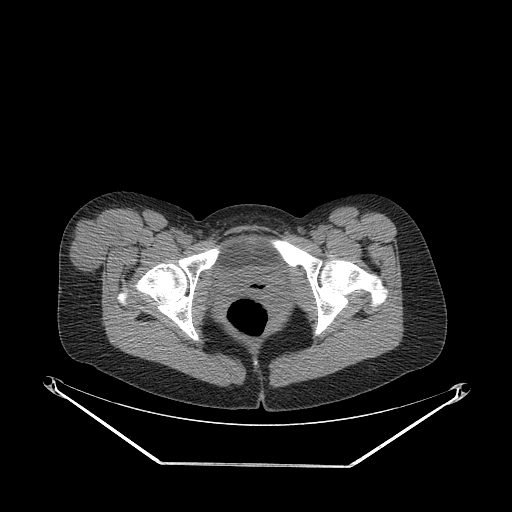
CT of an extremity soft-tissue mass (from a PET/CT study), one axial slice; slice 64 of 267 in the series (ordered by position); 140 kVp; soft-tissue window (W 400 / L 40 HU); 3.75 mm slice thickness; 512 × 512 image matrix. Female patient. From the clinical record (not read from this slice): histological type: synovial sarcoma; grade: intermediate; site of the primary tumour: right thigh.
Outlined on this slice (expert contour drawn on MRI and transferred to this co-registered scan by the dataset authors):
- gross tumour volume including surrounding oedema: bounding box [x1, y1, x2, y2] px = [69, 215, 122, 273]
- gross tumour volume (mass): [69, 215, 124, 273]